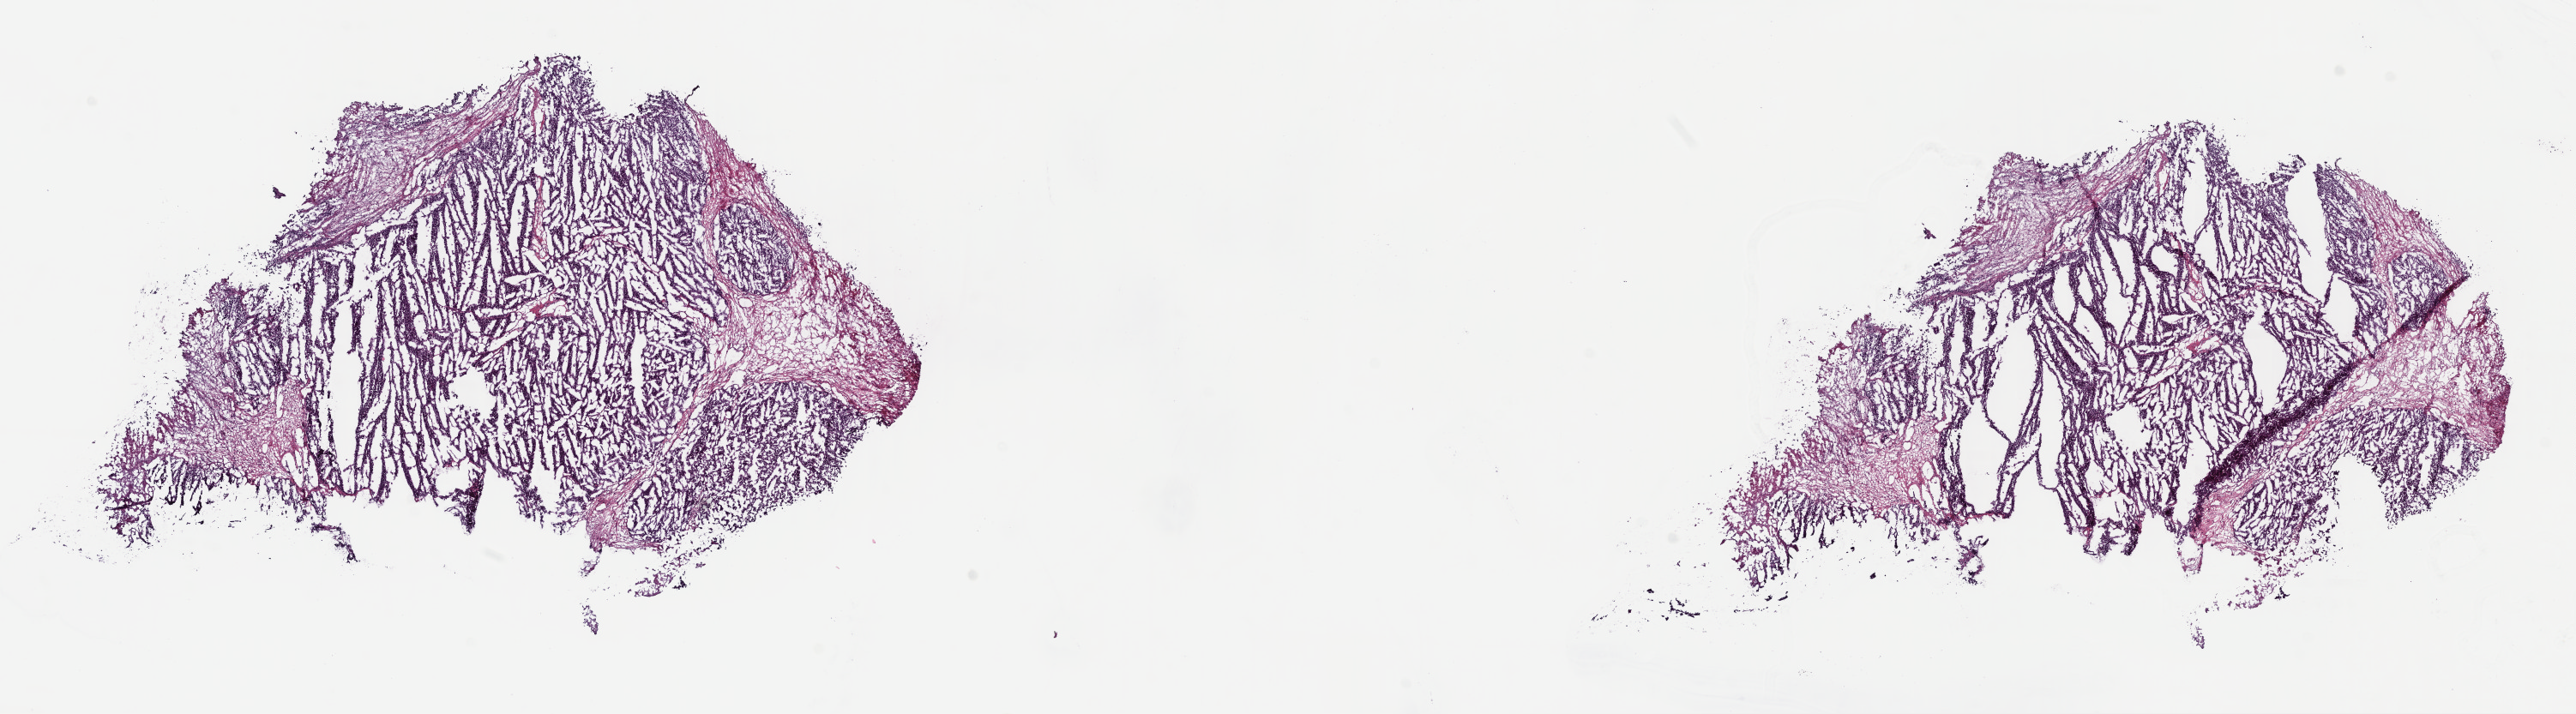
H&E-stained whole-slide image — shown as a low-resolution overview of the whole scanned area (about 23.6 x 6.5 mm). Frozen section from the top of the tissue portion. Adrenal cortex, primary tumour sample. Female, age 61 years at initial diagnosis. Pathologist review of this section (percent, as recorded): tumour cells 98%, tumour nuclei 88%, normal cells 0%, stromal cells 0%, necrosis 2%. Infiltration values recorded for this section: lymphocyte infiltration 0%, monocyte infiltration 0%, neutrophil infiltration 0%.
- lymph nodes positive (case pathology): 0 of 3 examined
- histologic diagnosis: Adrenal cortical carcinoma (cortex of adrenal gland)